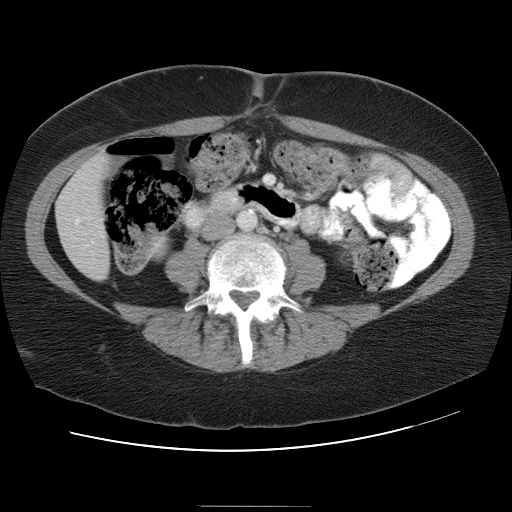
Contrast-enhanced abdominal CT, one axial slice. Intravenous contrast given. Soft-tissue window (W 400 / L 40 HU). 7.5 mm slice thickness. 512 × 512 image matrix. Female patient, age 52 years. From the clinical record (not read from this slice): diagnosis: colorectal cancer liver metastases, imaged before liver resection; multiple liver metastases: no; largest metastasis: 3 cm; disease in both lobes: yes.
Structures marked on this image (expert manual segmentation):
- hepatic veins: bounding box (x1, y1, x2, y2) in pixels: (75, 220, 78, 224)
- liver: (56, 154, 112, 280)